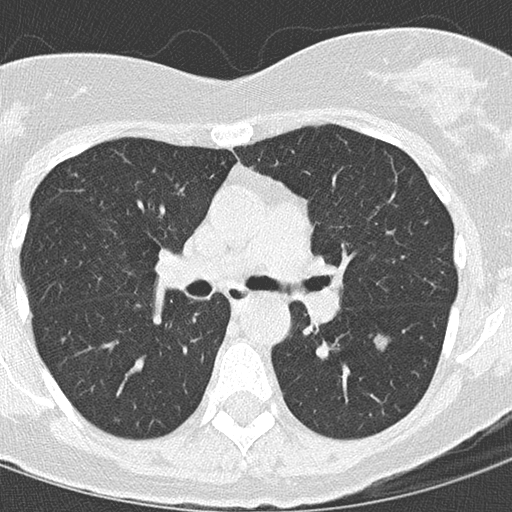
Chest CT (low-dose screening protocol), one axial image; baseline annual screen; lung window (W 1500 / L -600 HU). Female, age 68 years at enrolment.
Expert reader's lesion annotation, box from (x=366, y=320) to (x=412, y=367) px. The exam's reader record, not a measurement of the box and not confirmed to be the same lesion: non-calcified nodule or mass ≥4 mm, left lower lobe, 15 × 15 mm, mixed attenuation. Official screen result: positive, change unspecified: nodule(s) >= 4 mm or enlarging nodule(s), mass(es), or other non-specific abnormalities suspicious for lung cancer. Later outcome: lung cancer diagnosed 72 days after this screen — bronchiolo-alveolar adenocarcinoma, NOS, left lower lobe, stage IIIB (AJCC 6th edition), 12 mm at pathology.